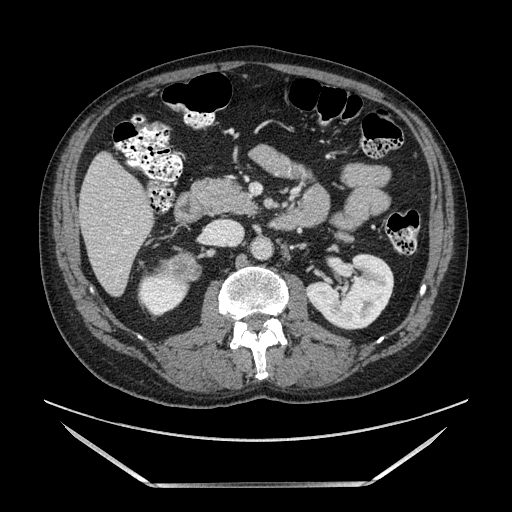
Contrast-enhanced abdominal CT, one axial slice; position 50 of 185 along the scan axis; soft-tissue window (W 400 / L 40 HU); 1.25 mm slice thickness; 512 × 512 image matrix, field of view 440 × 440 mm. Male patient. Case-level facts recorded for this patient, not image findings: diagnosis: adrenocortical carcinoma; tumour side: right adrenal; tumour size at pathology: 10.3 cm.
Annotated regions visible in this slice (semi-automatic segmentation, software-assisted and operator-edited):
- mass: bounding box <157,252,201,282> (left, top, right, bottom; pixels)